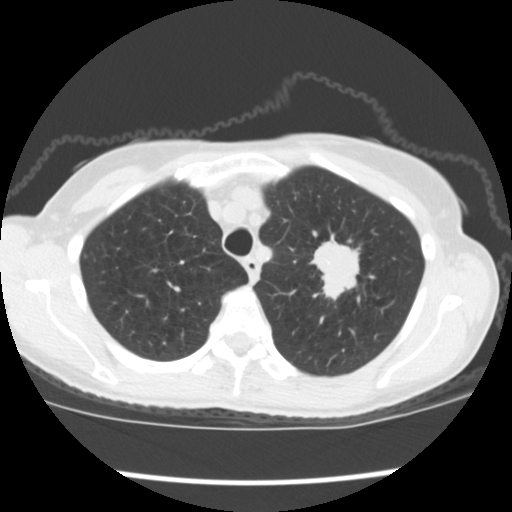
Low-dose screening chest CT, one axial slice. Slice 146 of 176 in the series (ordered by position). 120 kVp. Lung window (W 1500 / L -600 HU). 2.5 mm slice thickness. 512 × 512 image matrix, field of view 318 × 318 mm.
Annotated regions visible in this slice (outlined manually by an expert reader):
- lesion 1 (tumor, upper lobe of left lung): box from (x=311, y=235) to (x=360, y=300) px